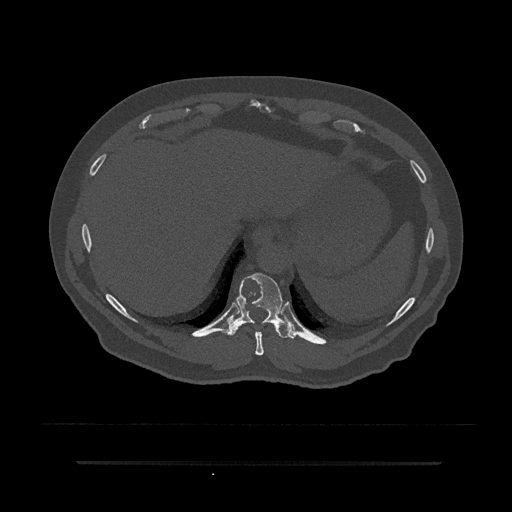
CT including the spine, one axial slice; reconstruction kernel Br40s/3; bone window (W 1800 / L 400 HU); 512 × 512 image matrix, field of view 464 × 464 mm. Patient: male, 59 years. Case-level facts recorded for this patient, not image findings: primary cancer: bile ducts.
Annotated regions visible in this slice (semi-automatically segmented with operator editing):
- T10 vertebra: bounding box (x1, y1, x2, y2) in pixels: (226, 273, 294, 339)
- T9 vertebra: (255, 331, 264, 356)